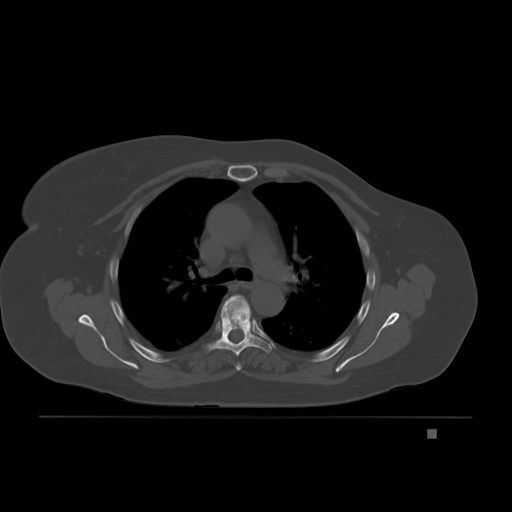
CT including the spine, one axial slice; slice 146 of 221 in the series (ordered by position); bone window (W 1800 / L 400 HU); 512 × 512 image matrix, field of view 474 × 474 mm. Female patient, age 63 years. From the clinical record (not read from this slice): primary cancer: breast.
Annotated regions visible in this slice (semi-automatic segmentation, software-assisted and operator-edited):
- T4 vertebra: bounding box <236,363,241,371> (left, top, right, bottom; pixels)
- T5 vertebra: <207,295,272,356>